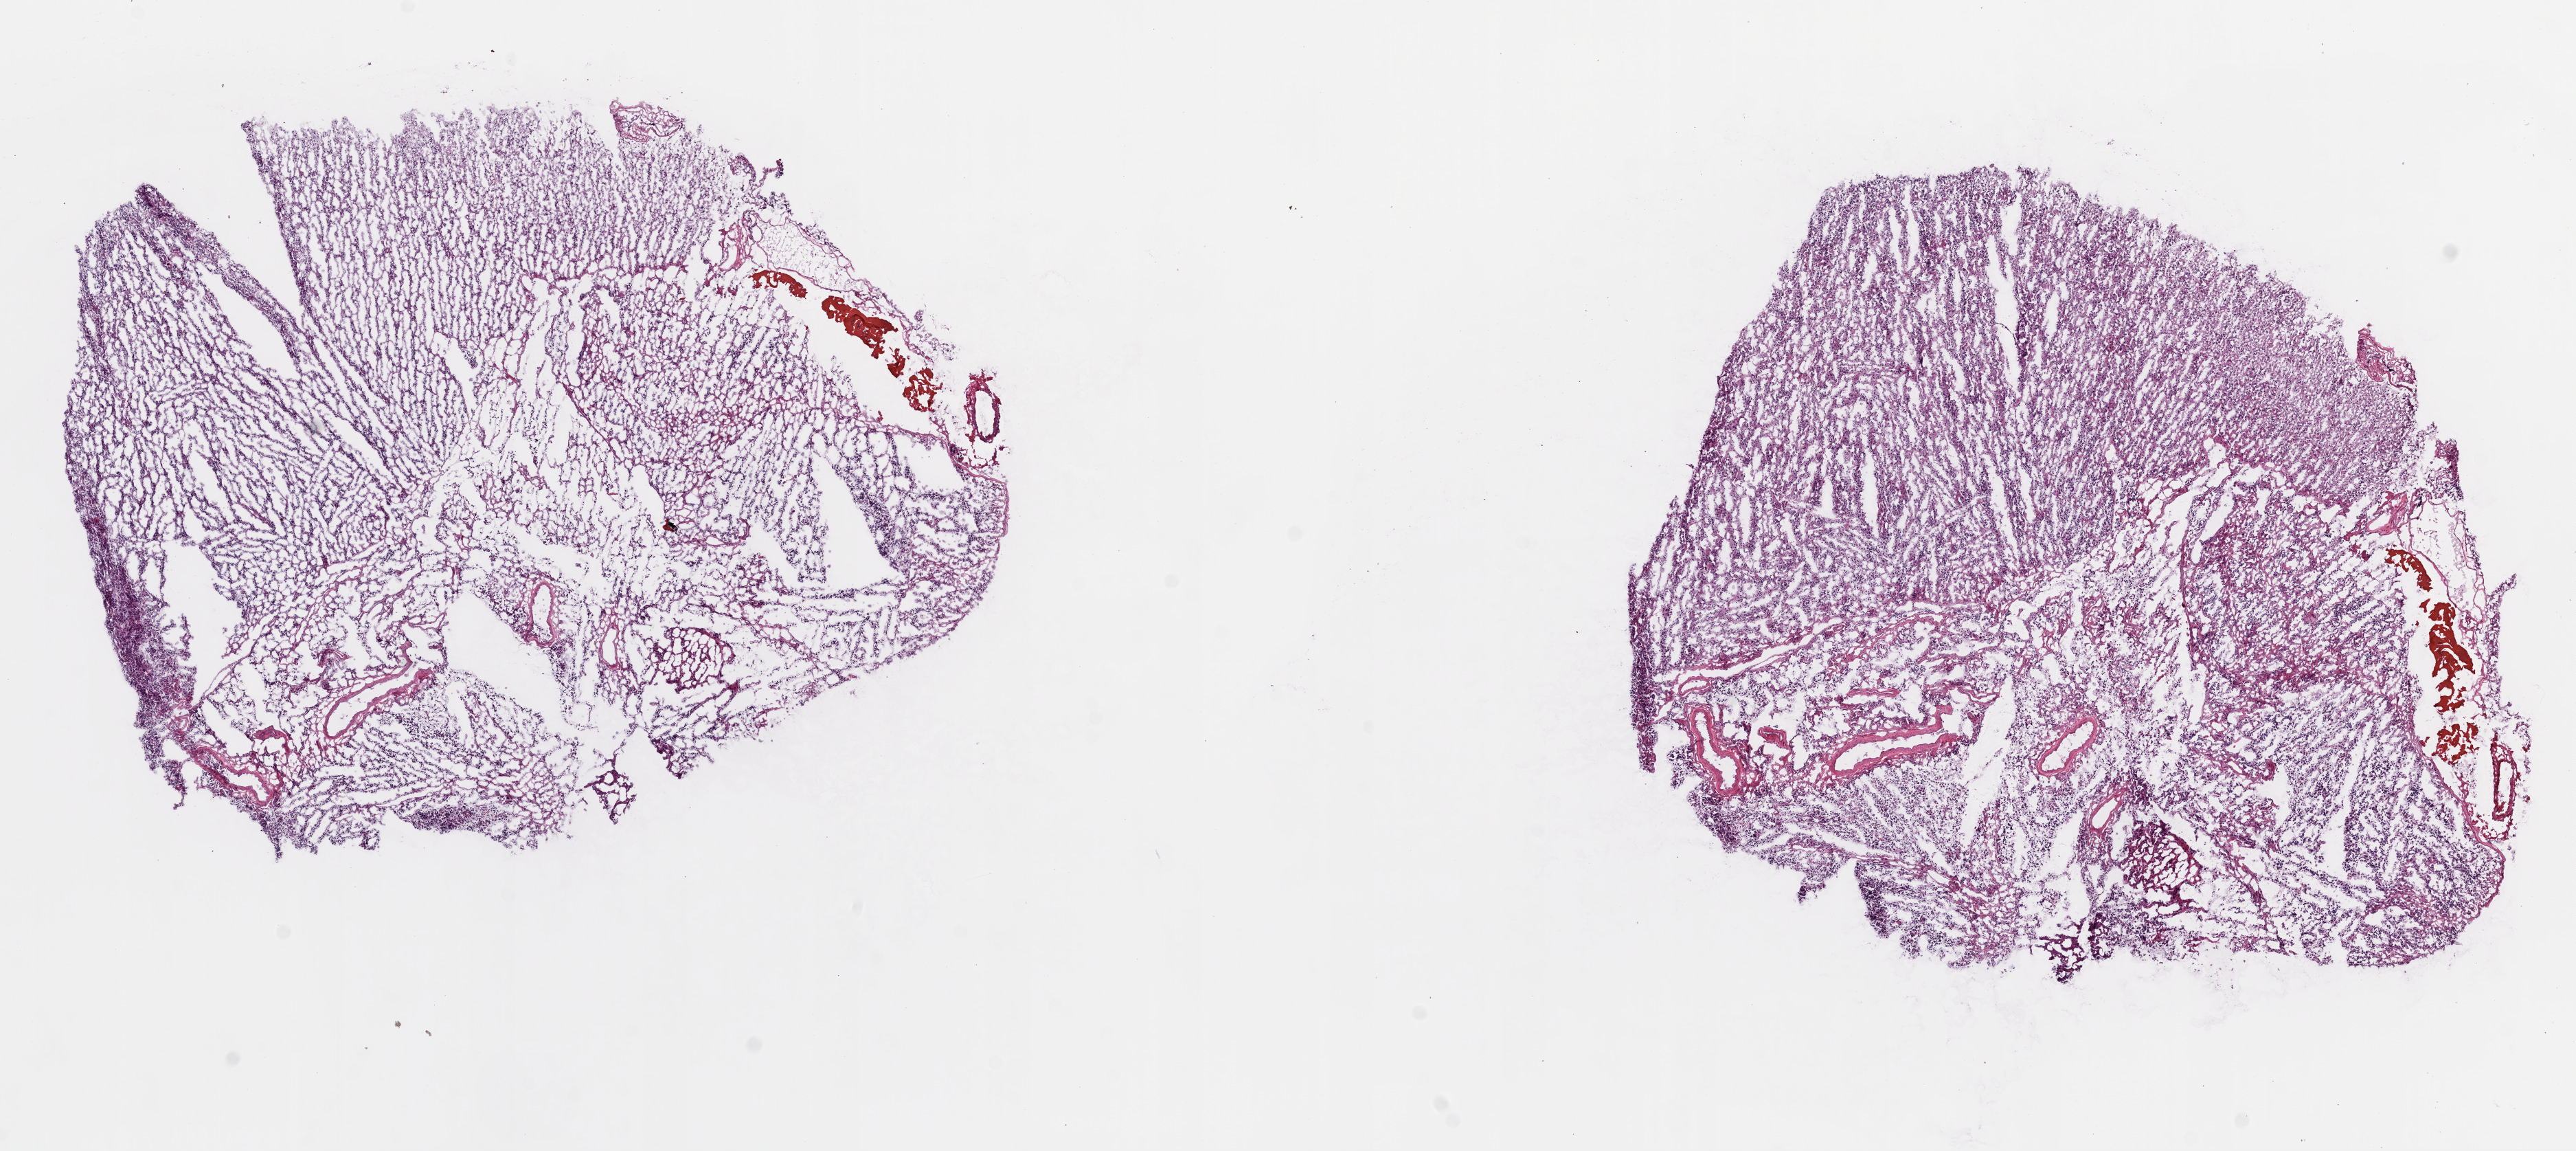
Digitized H&E tissue section (whole slide) — shown as a low-resolution overview of the whole scanned area (about 15.0 x 6.7 mm, acquisition: 20x scan). Frozen section. Brain, primary tumour sample. Female, age 38 years at initial diagnosis. Histologic grade: G3 (poorly differentiated). Composition of this section per pathologist review: tumour cells 100%, tumour nuclei 75%, normal cells 0%, stromal cells 0%, necrosis 0%.
Diagnosis: Mixed glioma (cerebrum).